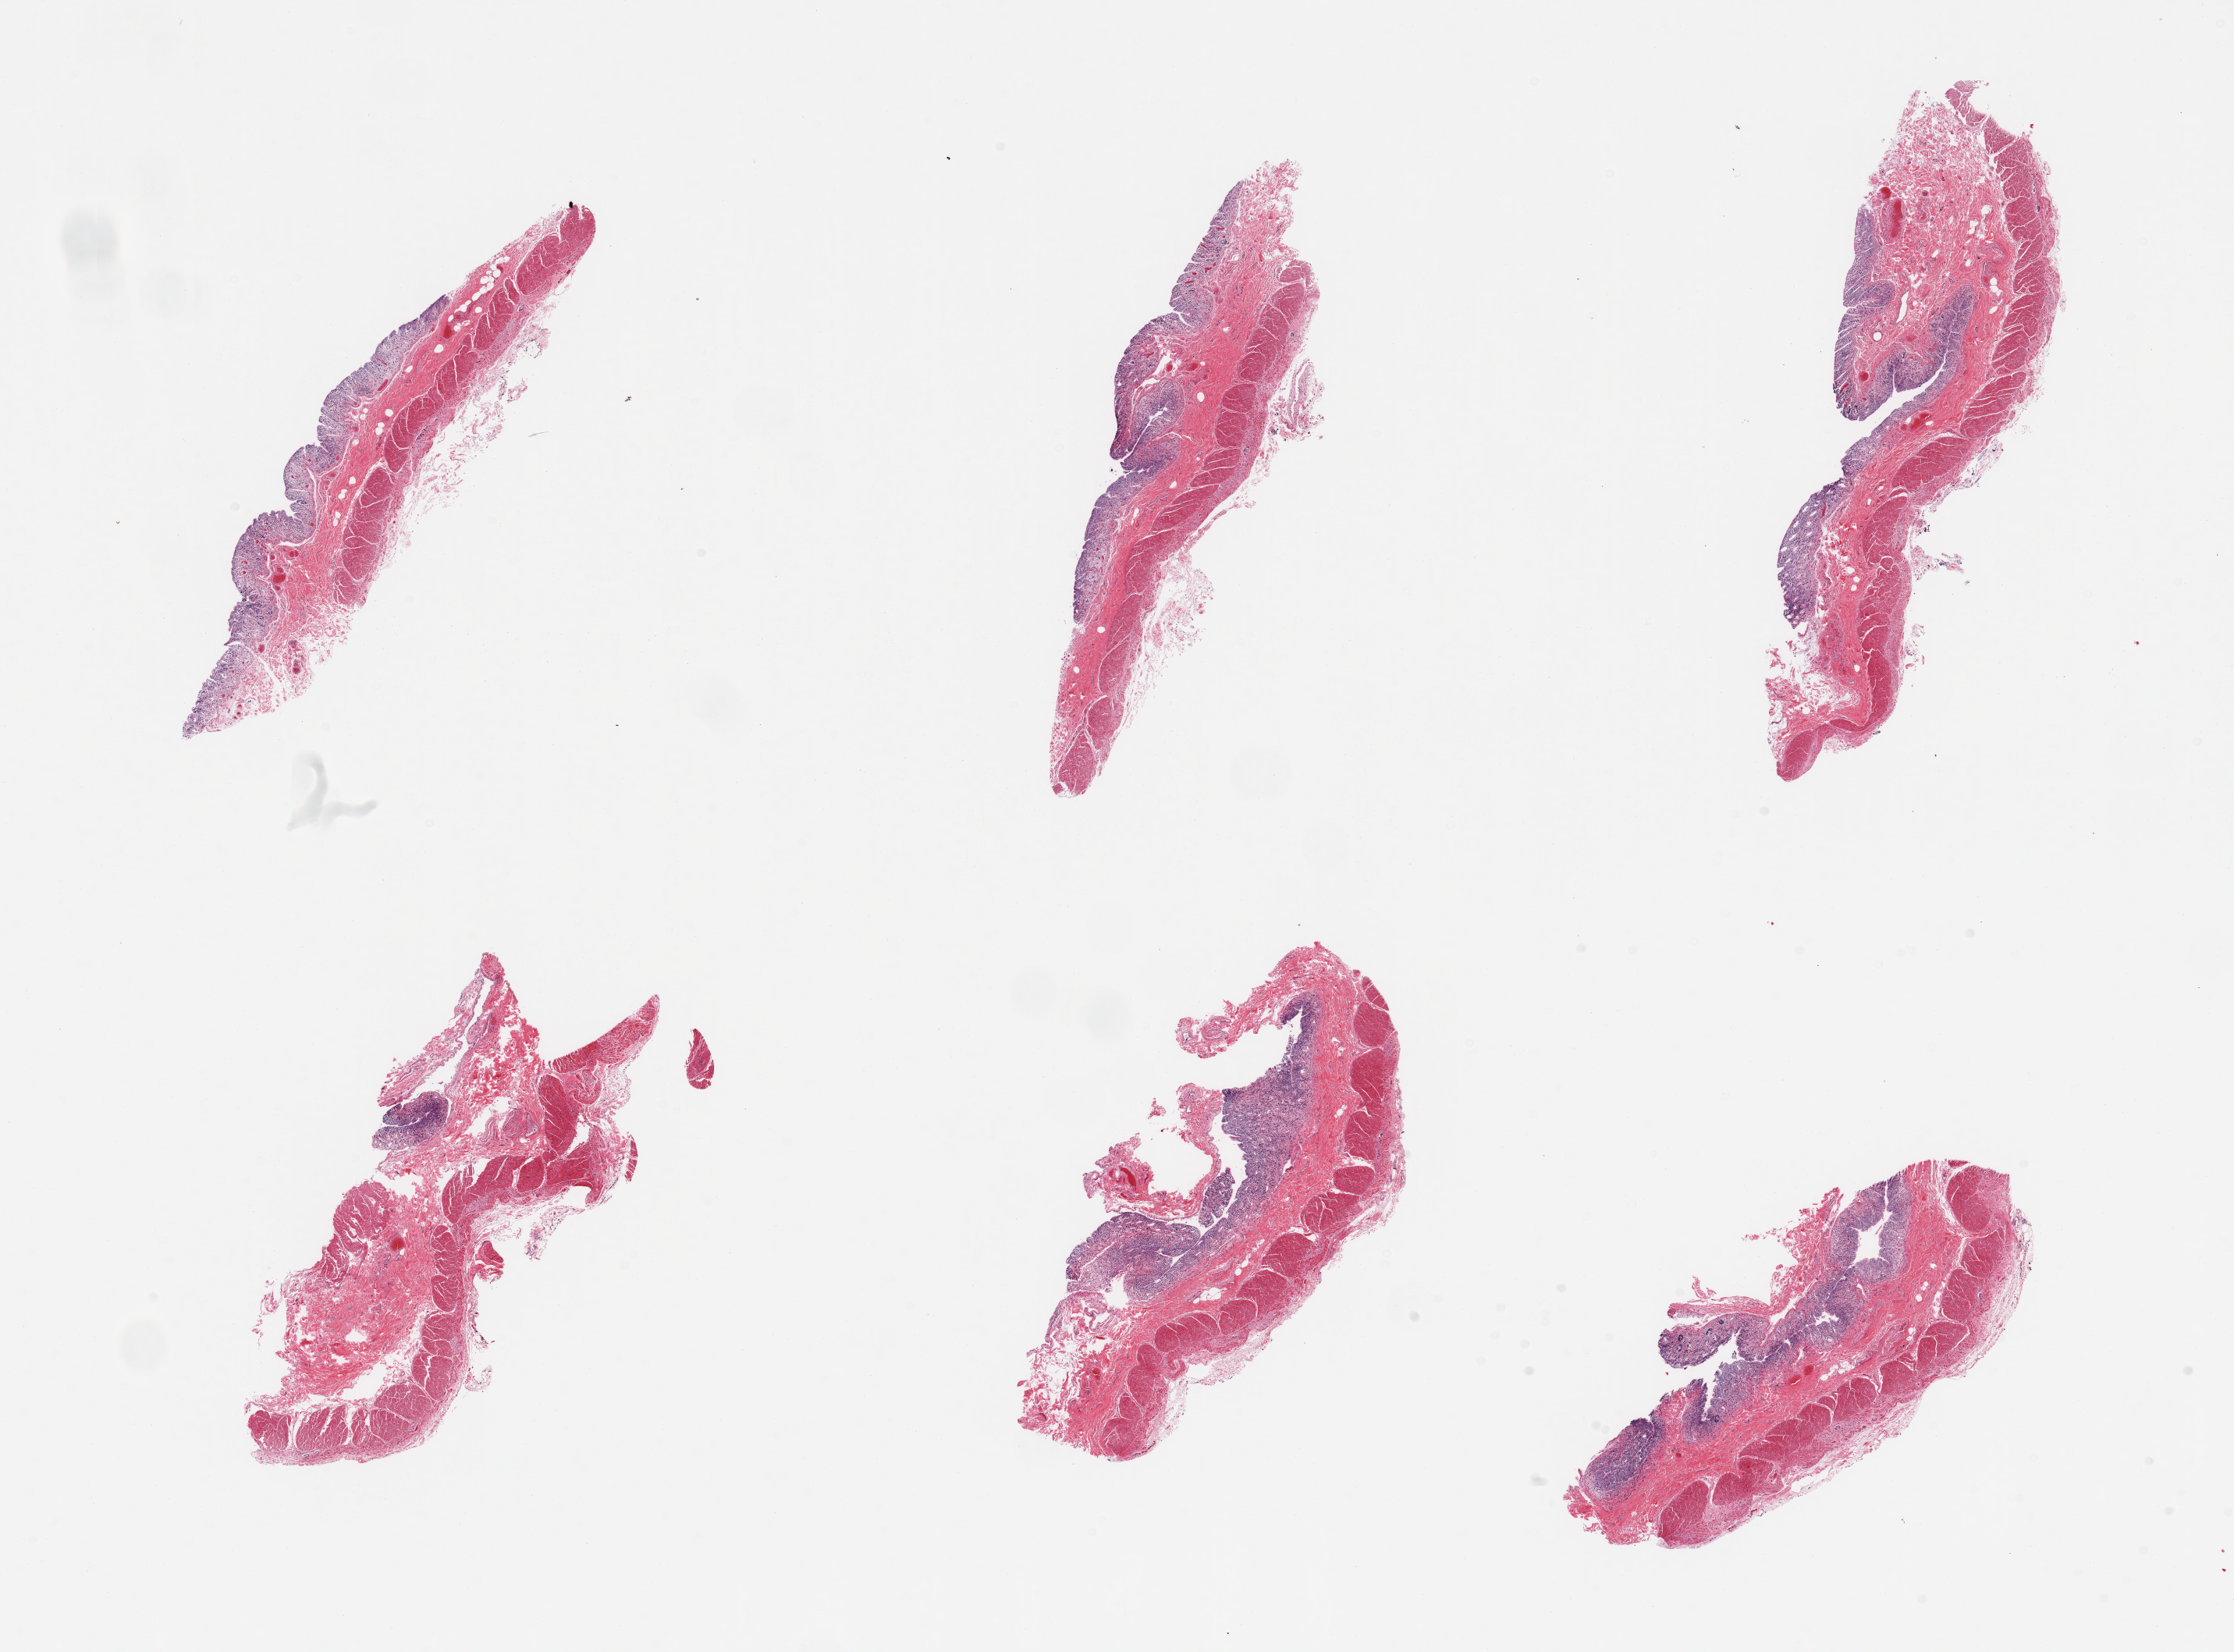
H&E whole-slide image, shown as a low-resolution overview of the whole scanned area (about 22.6 x 16.7 mm, from a 20x scan). PAXgene-fixed, paraffin-embedded tissue. Section of transverse colon (target tissue). Donor tissue sample. Male donor.
• pathologist's review note for this sample: 6 pieces; autolyzed mucosa and muscularis